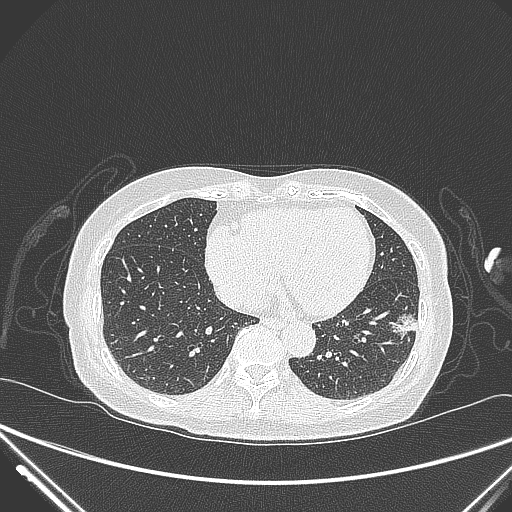
Chest CT, one axial slice. 120 kVp. Lung window (W 1500 / L -600 HU). 1 mm slice thickness. 512 × 512 image matrix, field of view 377 × 377 mm. Patient: female, 82 years. From the clinical record (not read from this slice): clinical TNM (as recorded): T1c N0 M0.
Structures marked on this image (bounding box drawn by a radiologist):
- lung tumour (recorded histology: adenocarcinoma): bounding box <387,302,425,349> (left, top, right, bottom; pixels)